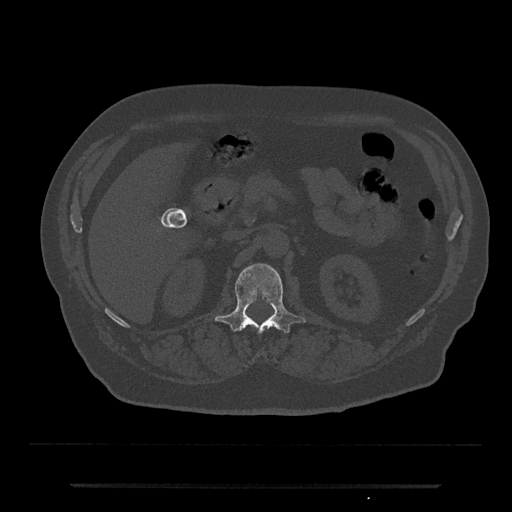
CT including the spine, one axial slice; position 541 of 797 along the scan axis; reconstruction kernel Br40s/3; 120 kVp; bone window (W 1800 / L 400 HU); 512 × 512 image matrix, field of view 434 × 434 mm. Male patient, age 80 years. Case-level facts recorded for this patient, not image findings: primary cancer: prostate.
Structures marked on this image (semi-automatic segmentation, software-assisted and operator-edited):
- L1 vertebra: bounding box <214,263,306,357> (left, top, right, bottom; pixels)